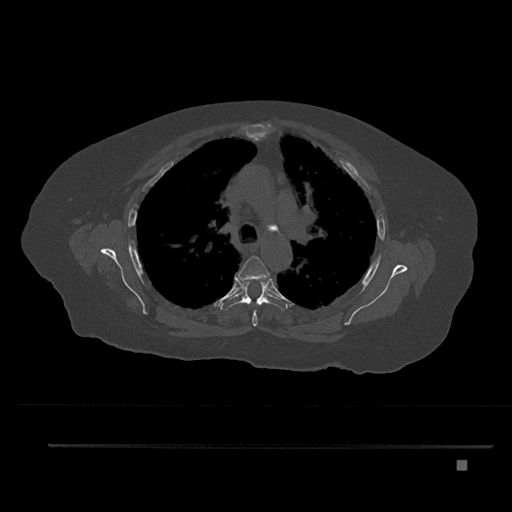
CT including the spine, one axial slice. Slice 581 of 797 in the series (ordered by position). Bone window (W 1800 / L 400 HU). 512 × 512 image matrix, field of view 437 × 437 mm. Female patient, age 76 years. From the clinical record (not read from this slice): primary cancer: lung.
Annotated regions visible in this slice (semi-automatically segmented with operator editing):
- T4 vertebra: box from (x=235, y=256) to (x=270, y=326) px
- T5 vertebra: (x=220, y=279)–(x=288, y=311)